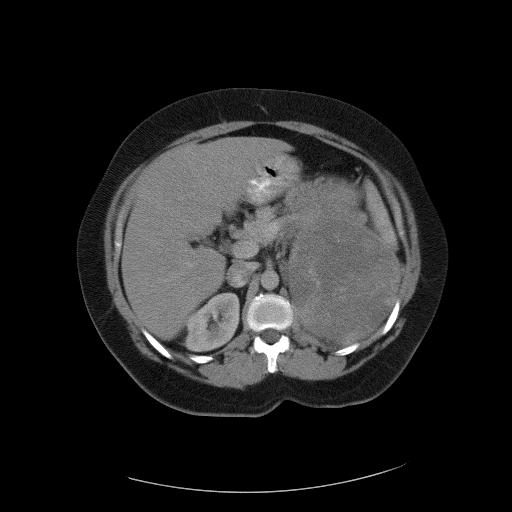
Contrast-enhanced abdominal CT, one axial slice. Position 67 of 90 along the scan axis. Reconstruction kernel FC01. 120 kVp. Intravenous contrast given. Soft-tissue window (W 400 / L 40 HU). 512 × 512 image matrix. Female patient, age 55 years. Case-level facts recorded for this patient, not image findings: diagnosis: adrenocortical carcinoma; tumour side: left adrenal; tumour size at pathology: 22 cm; Ki-67 index: 10 %; stage (as recorded): 3.
Outlined on this slice (semi-automatically segmented with operator editing):
- mass: bounding box <289,200,400,342> (left, top, right, bottom; pixels)